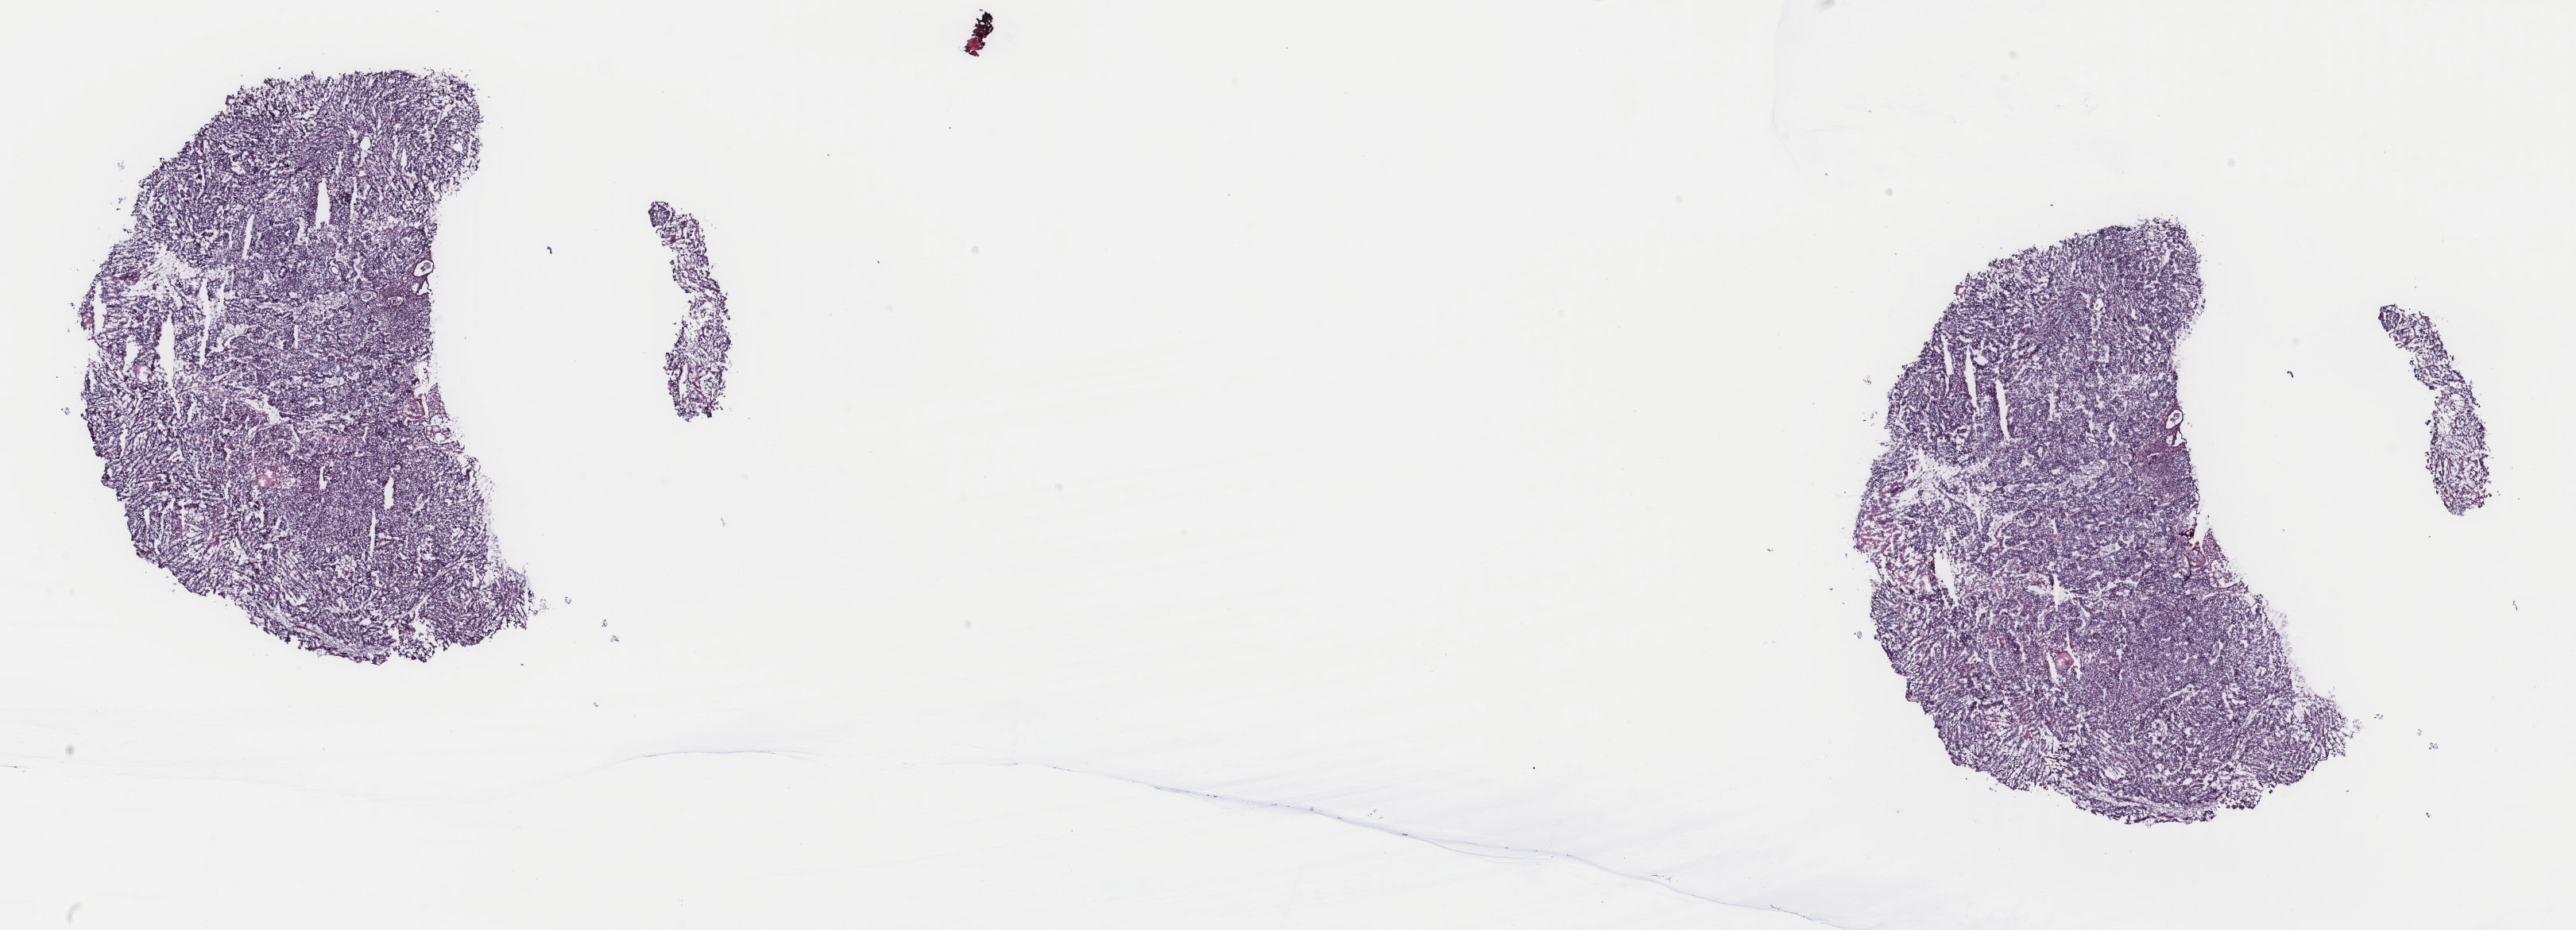
Whole-slide histology image, H&E-stained, whole scanned area (about 25.7 x 9.3 mm, from a 40x scan) shown as a low-resolution overview, frozen section from the top of the tissue portion, primary tumour sample from the uterus. Female patient; age at initial diagnosis 68 years. Pathologist review of this section (percent, as recorded): tumour cells 80%, tumour nuclei 90%, normal cells 0%, stromal cells 0%, necrosis 20%. Infiltration values recorded for this section: lymphocyte infiltration 0%, monocyte infiltration 0%, neutrophil infiltration 0%.
Diagnosis: Mullerian mixed tumor. FIGO stage: IA.